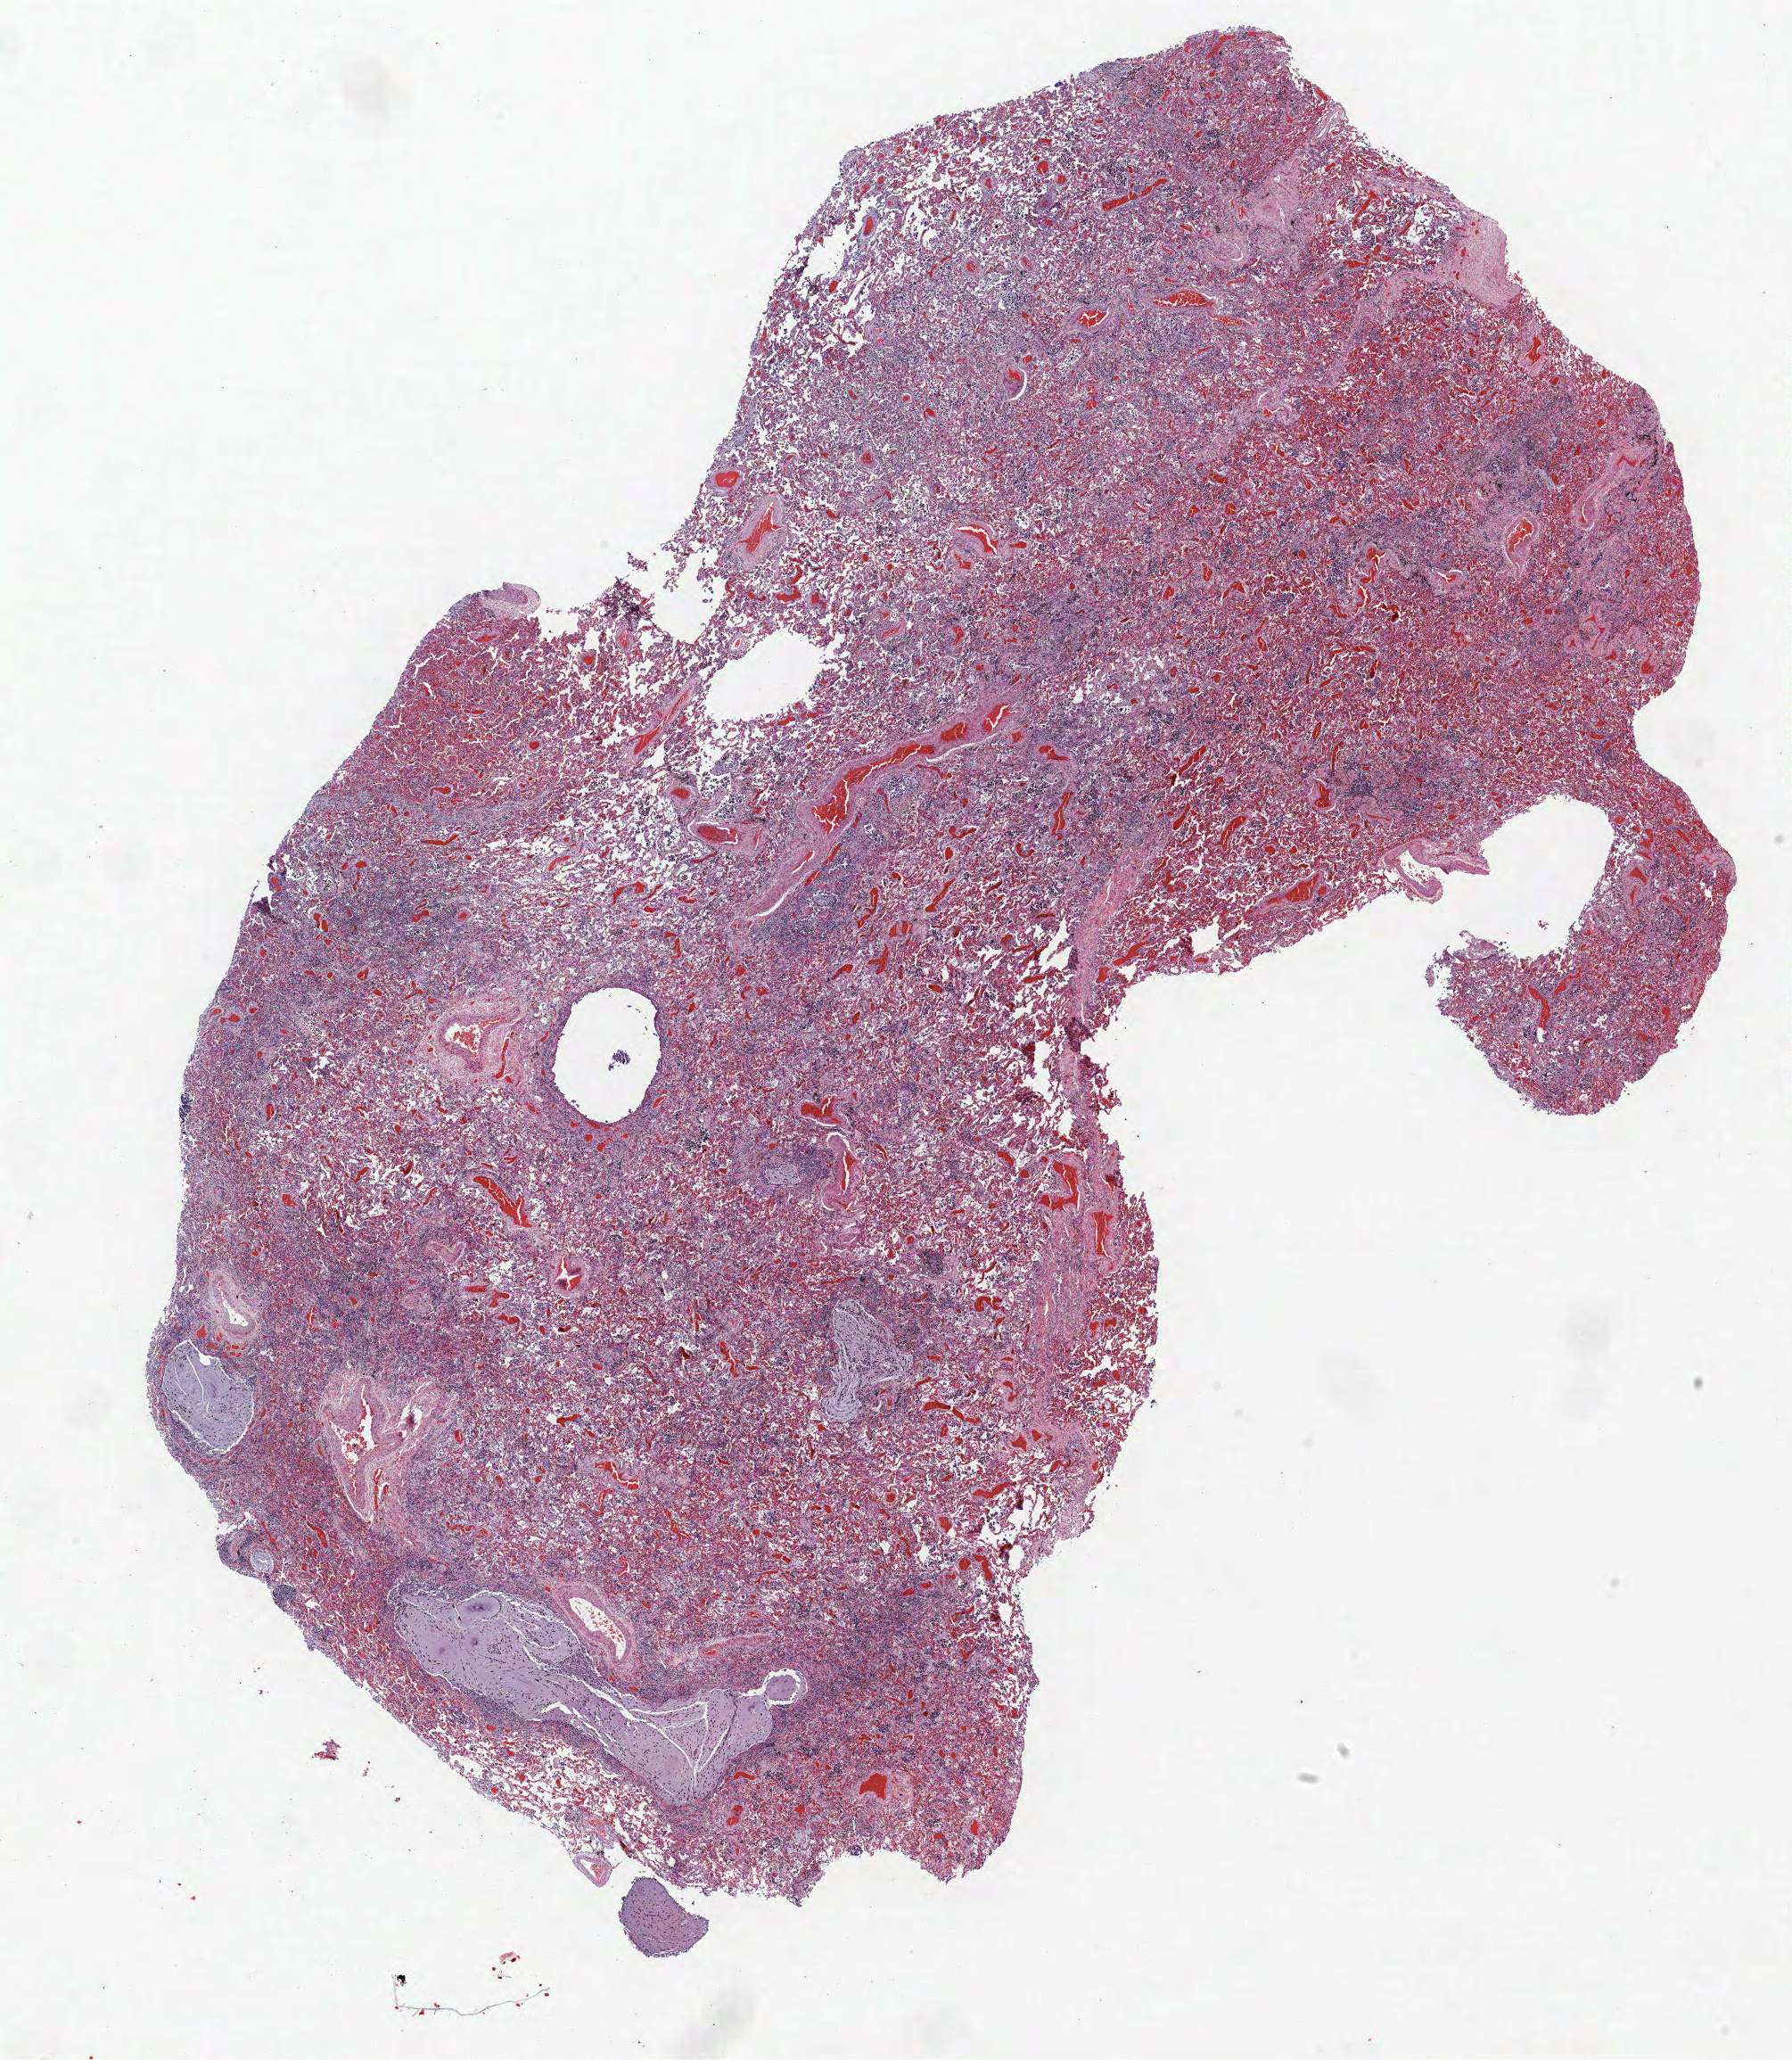
Hematoxylin and eosin (H&E) stained whole-slide image, whole scanned area (about 16.1 x 18.5 mm, acquisition: 40x scan) shown as a low-resolution overview; FFPE section; lung tissue. Female, age 61 at enrolment. Current smoker at enrolment. Grade: well differentiated (G1).
Participant's lung-cancer diagnosis: Adenocarcinoma, NOS. Primary tumour location (clinical record): right upper lobe. Stage (AJCC 6th edition): IIIB. Tumour size (pathology): 30 mm. Note: participant had 2 primary lung cancers recorded; fields above describe the first.